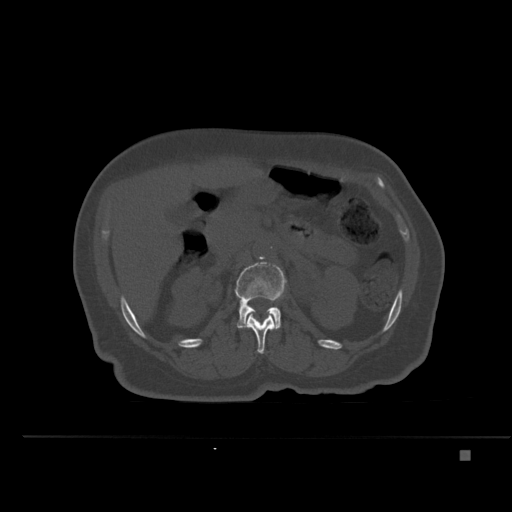
CT including the spine, one axial slice. Bone window (W 1800 / L 400 HU). 1.5 mm slice thickness. 512 × 512 image matrix, field of view 422 × 422 mm. Patient: female, 74 years. From the clinical record (not read from this slice): primary cancer: colon.
Annotated regions visible in this slice (semi-automatically segmented with operator editing):
- L1 vertebra: box from (x=246, y=312) to (x=276, y=354) px
- L2 vertebra: (x=235, y=261)–(x=286, y=329)